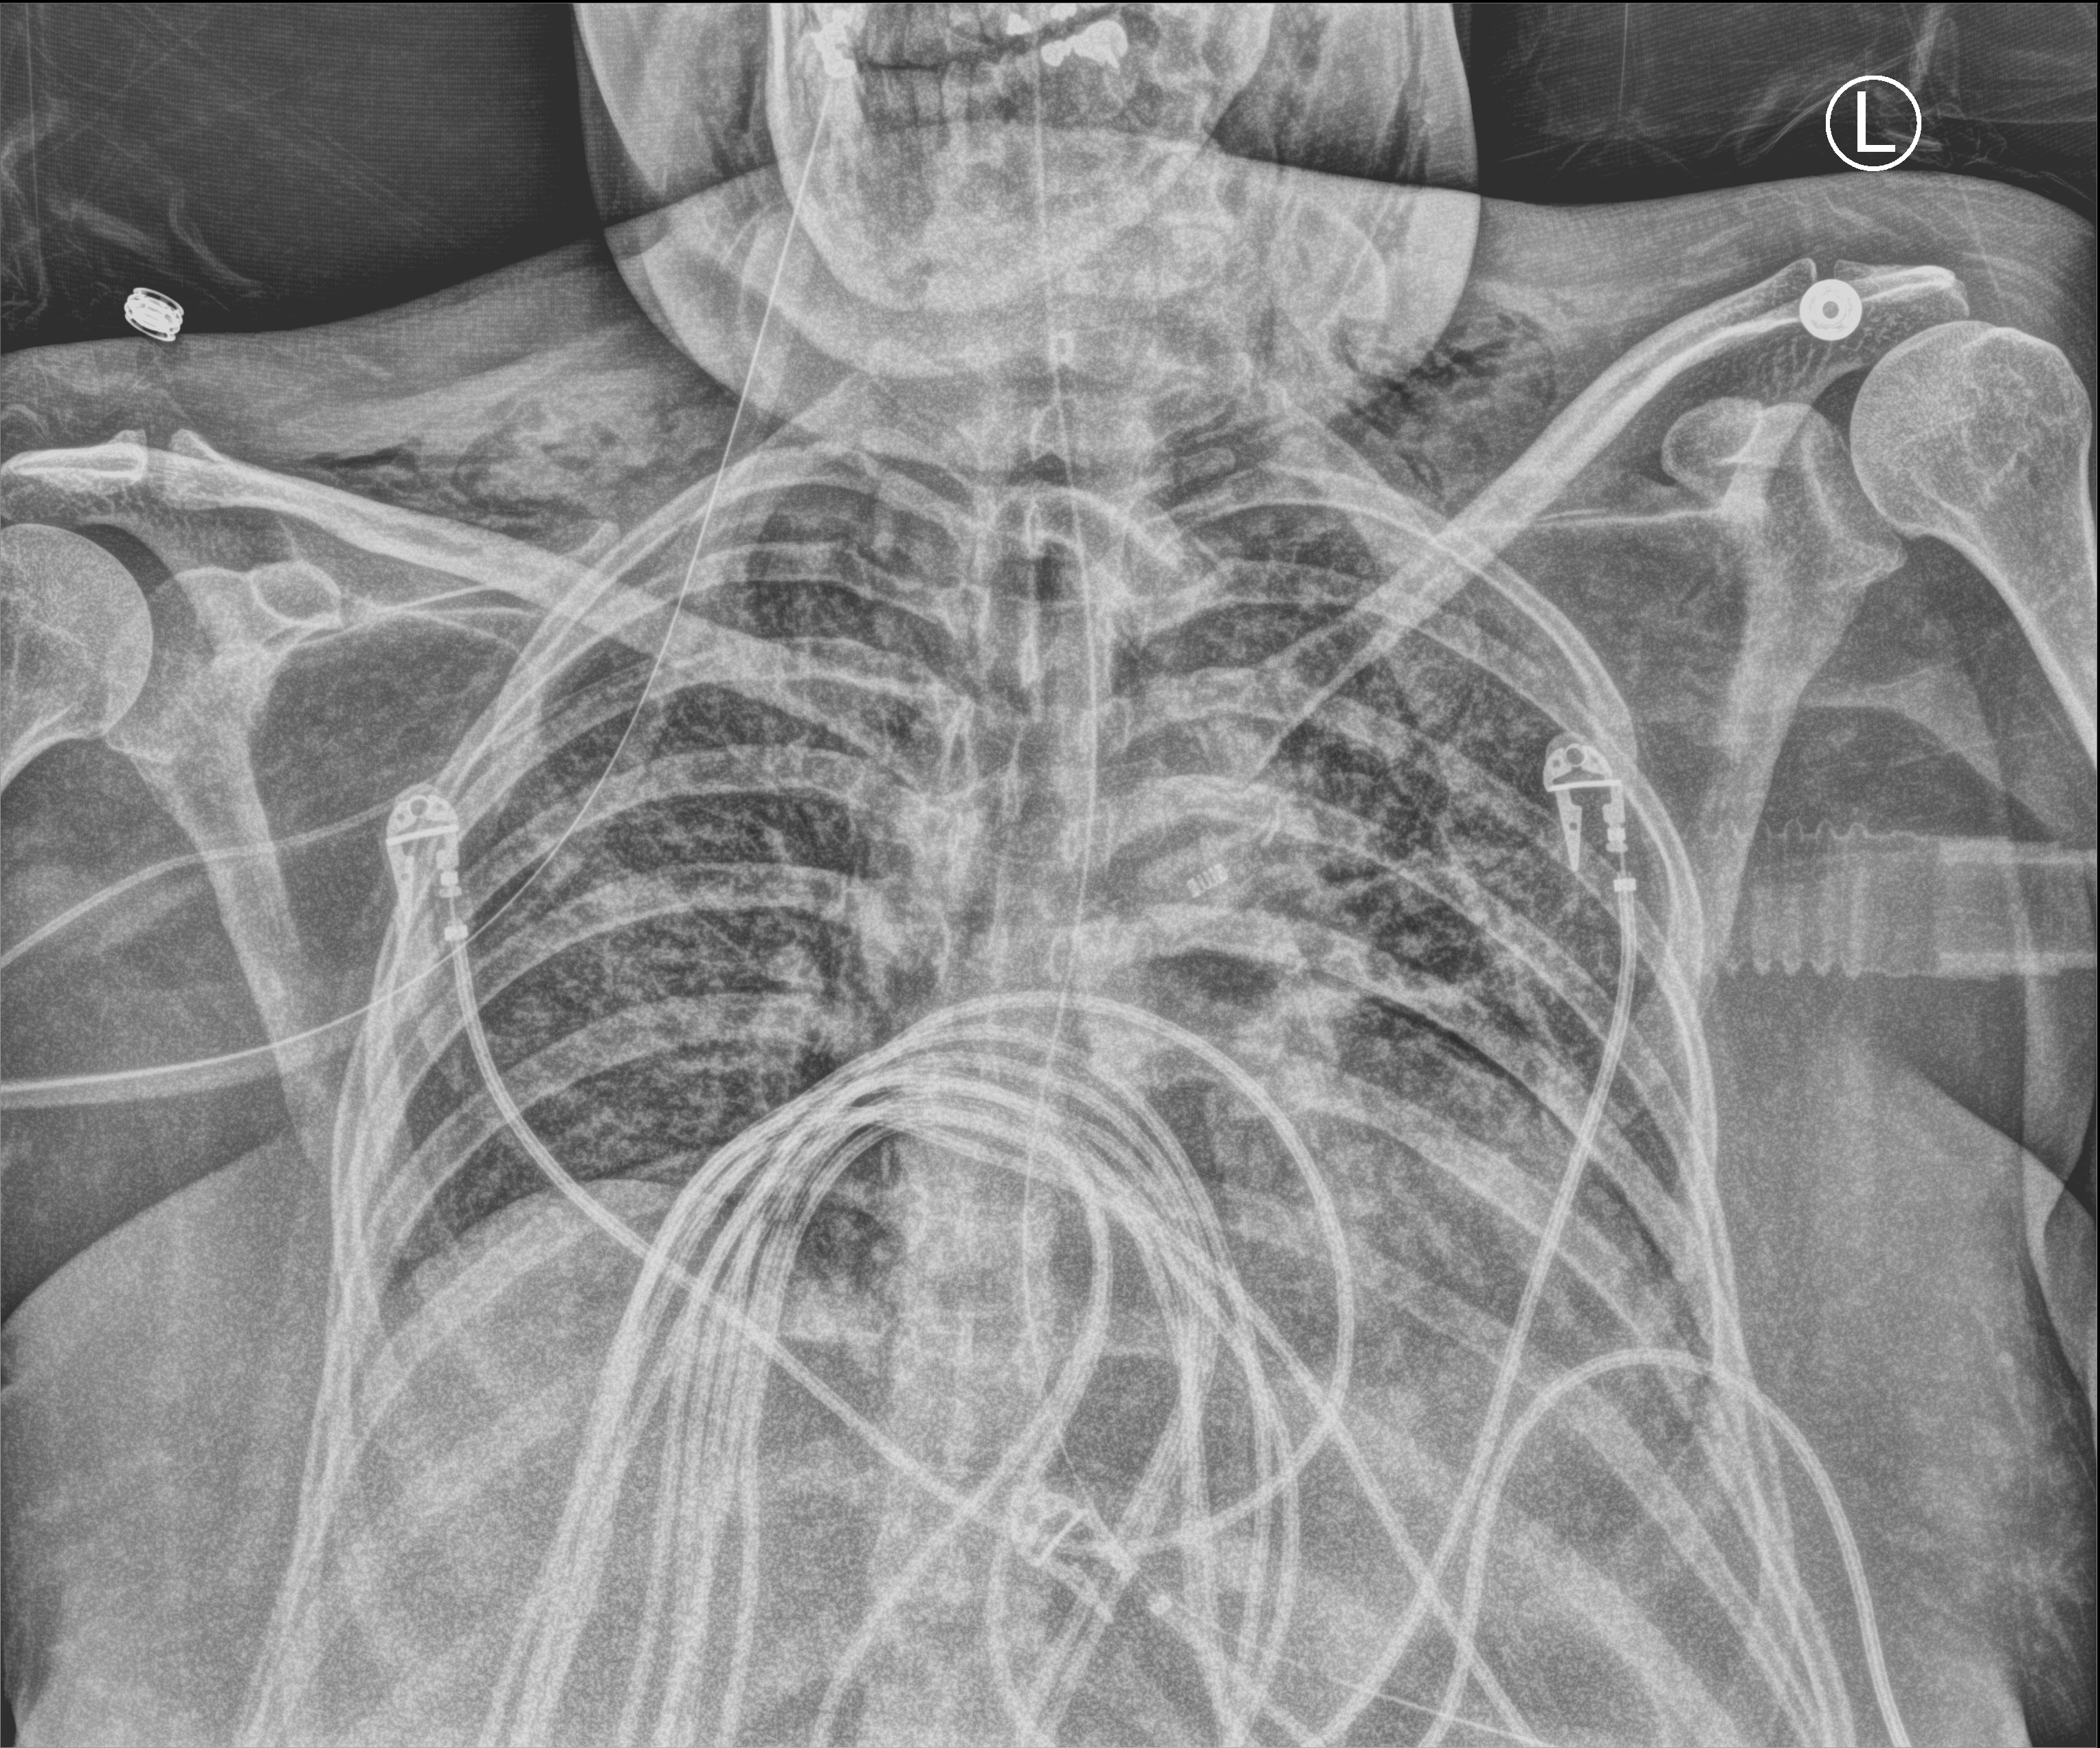
Bedside chest radiograph (computed radiography); anteroposterior (AP) projection. Patient hospitalised with COVID-19; female, aged 18–59 years.
From the hospital-stay record, not from the radiograph (when in the stay this image was taken is not recorded):
- length of hospital stay: 73 days
- mechanically ventilated during this hospital stay: yes
- admitted to intensive care during this hospital stay: yes